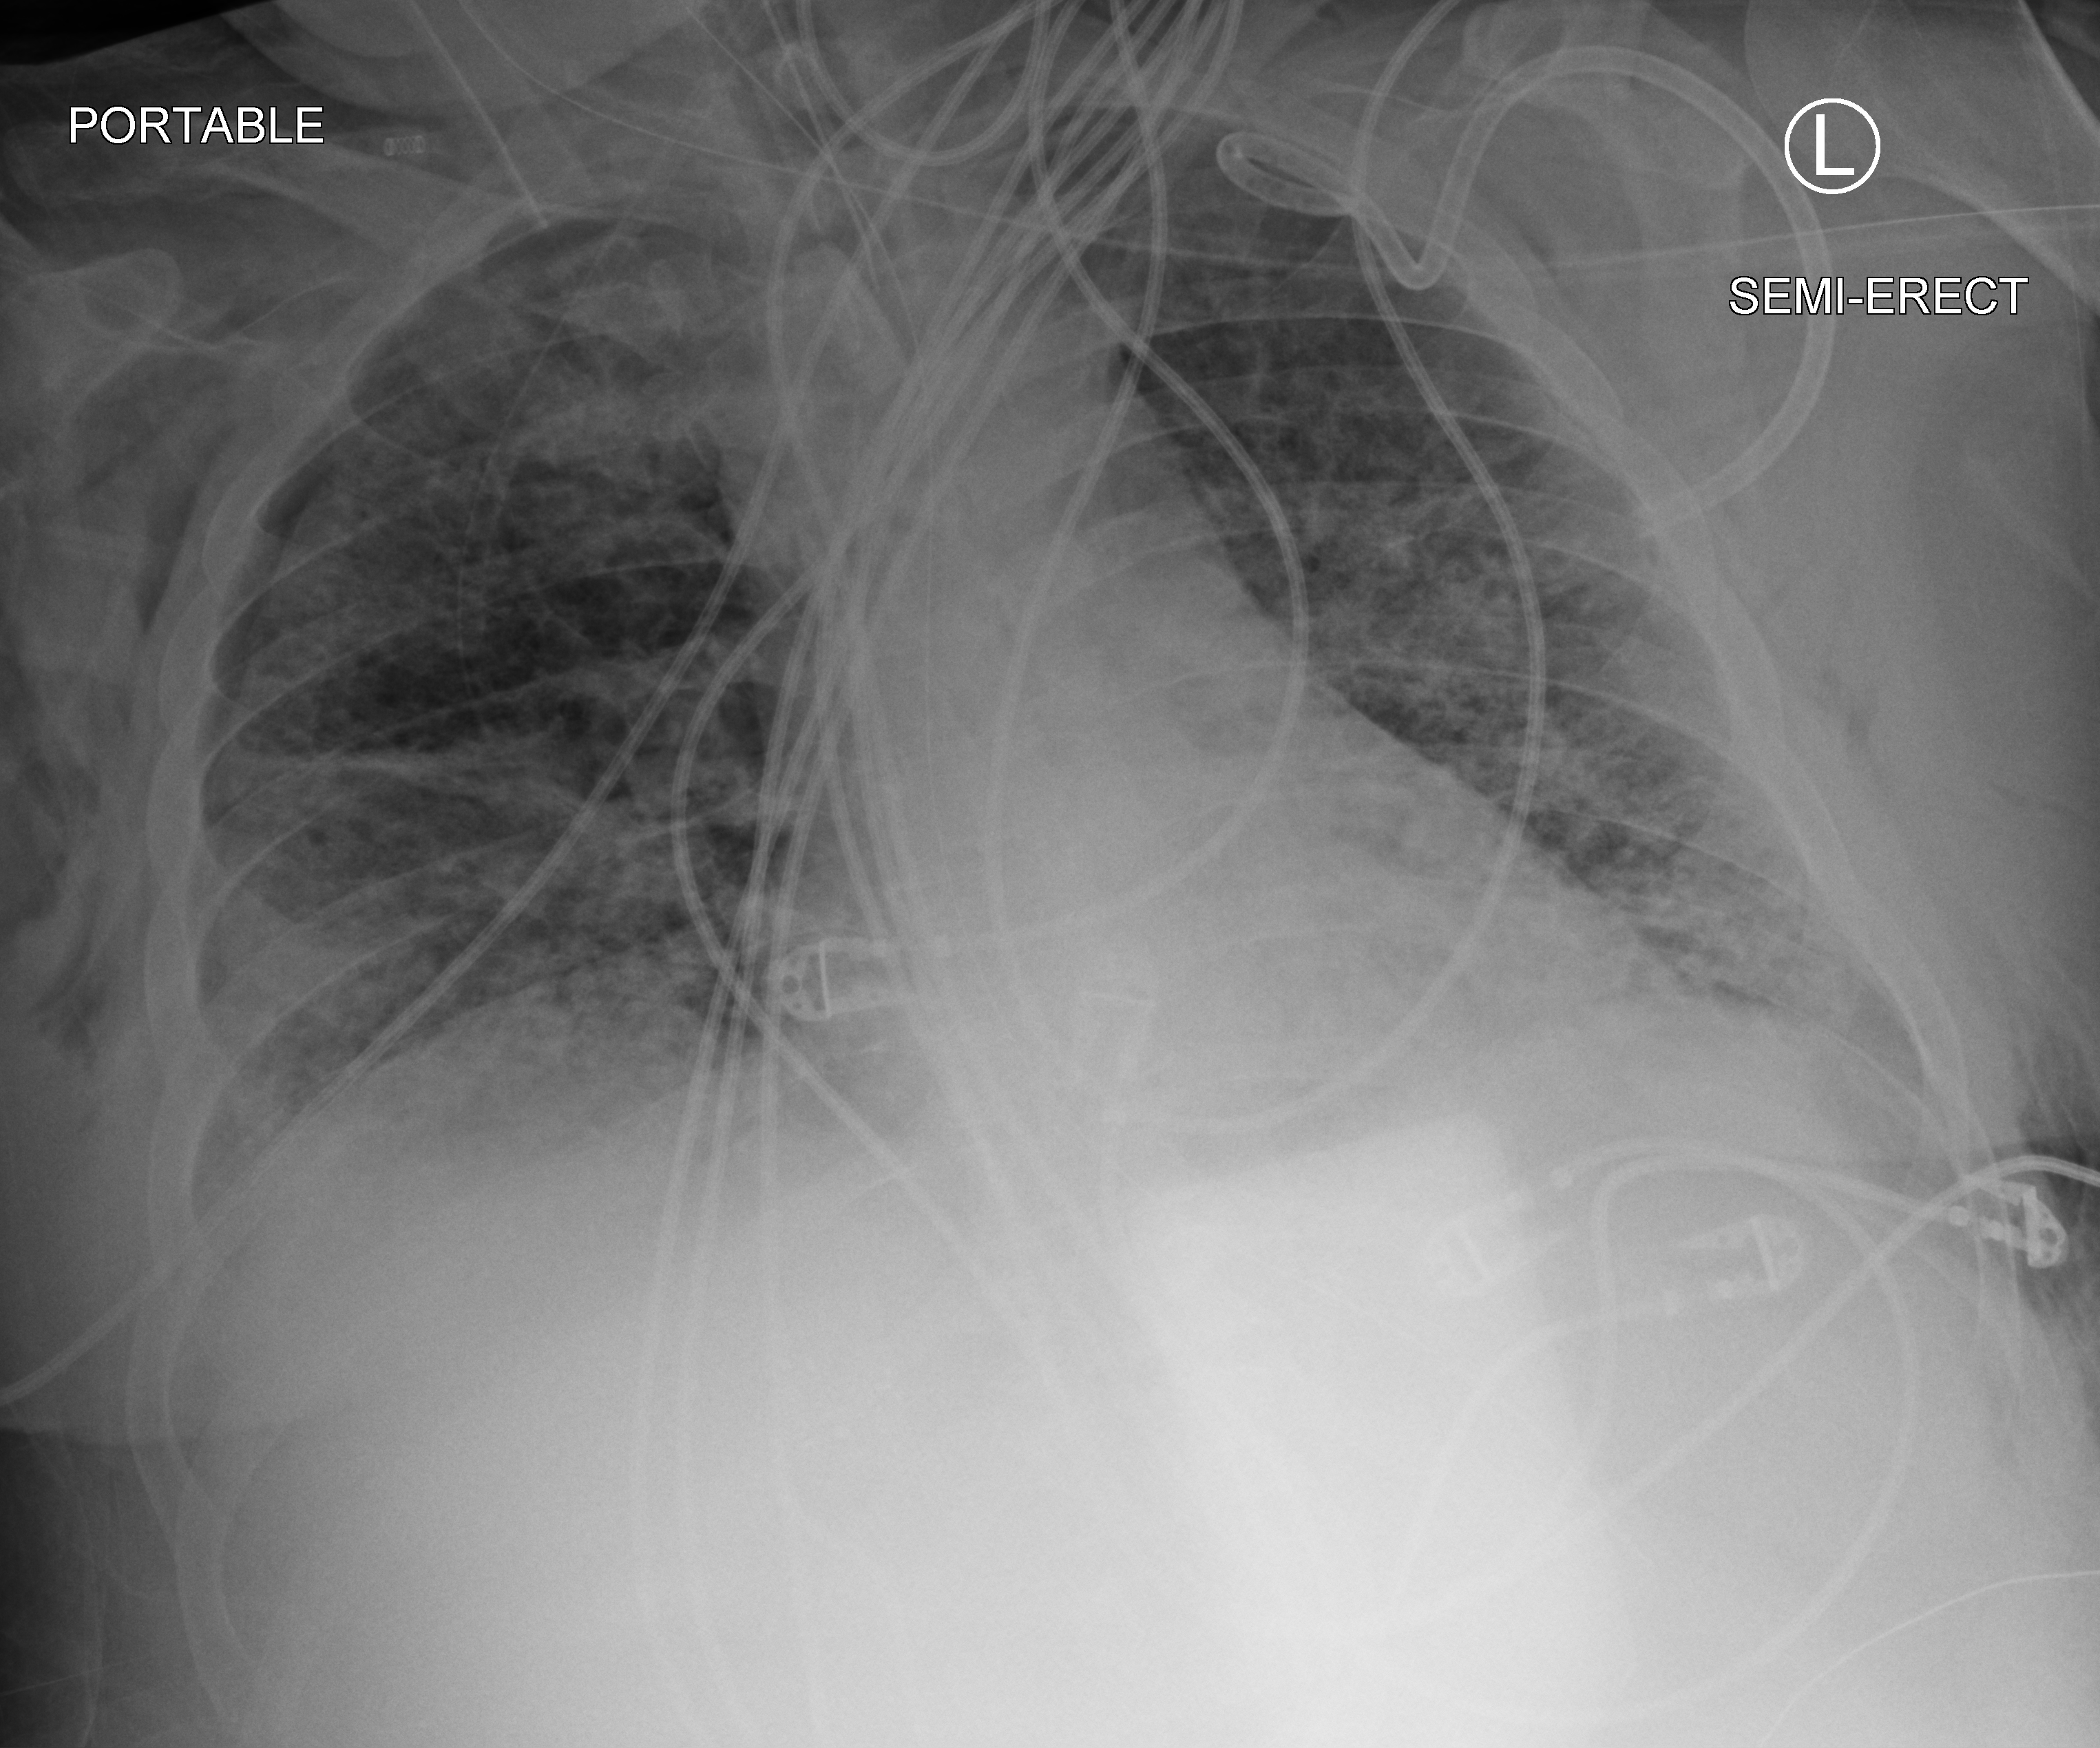
Bedside chest radiograph (computed radiography); anteroposterior (AP) projection. Patient hospitalised with COVID-19, aged 18–59 years.
Admission-level facts for this patient (not findings on this image; timing relative to this image not recorded):
- admitted to intensive care during this hospital stay: yes
- length of hospital stay: 31 days